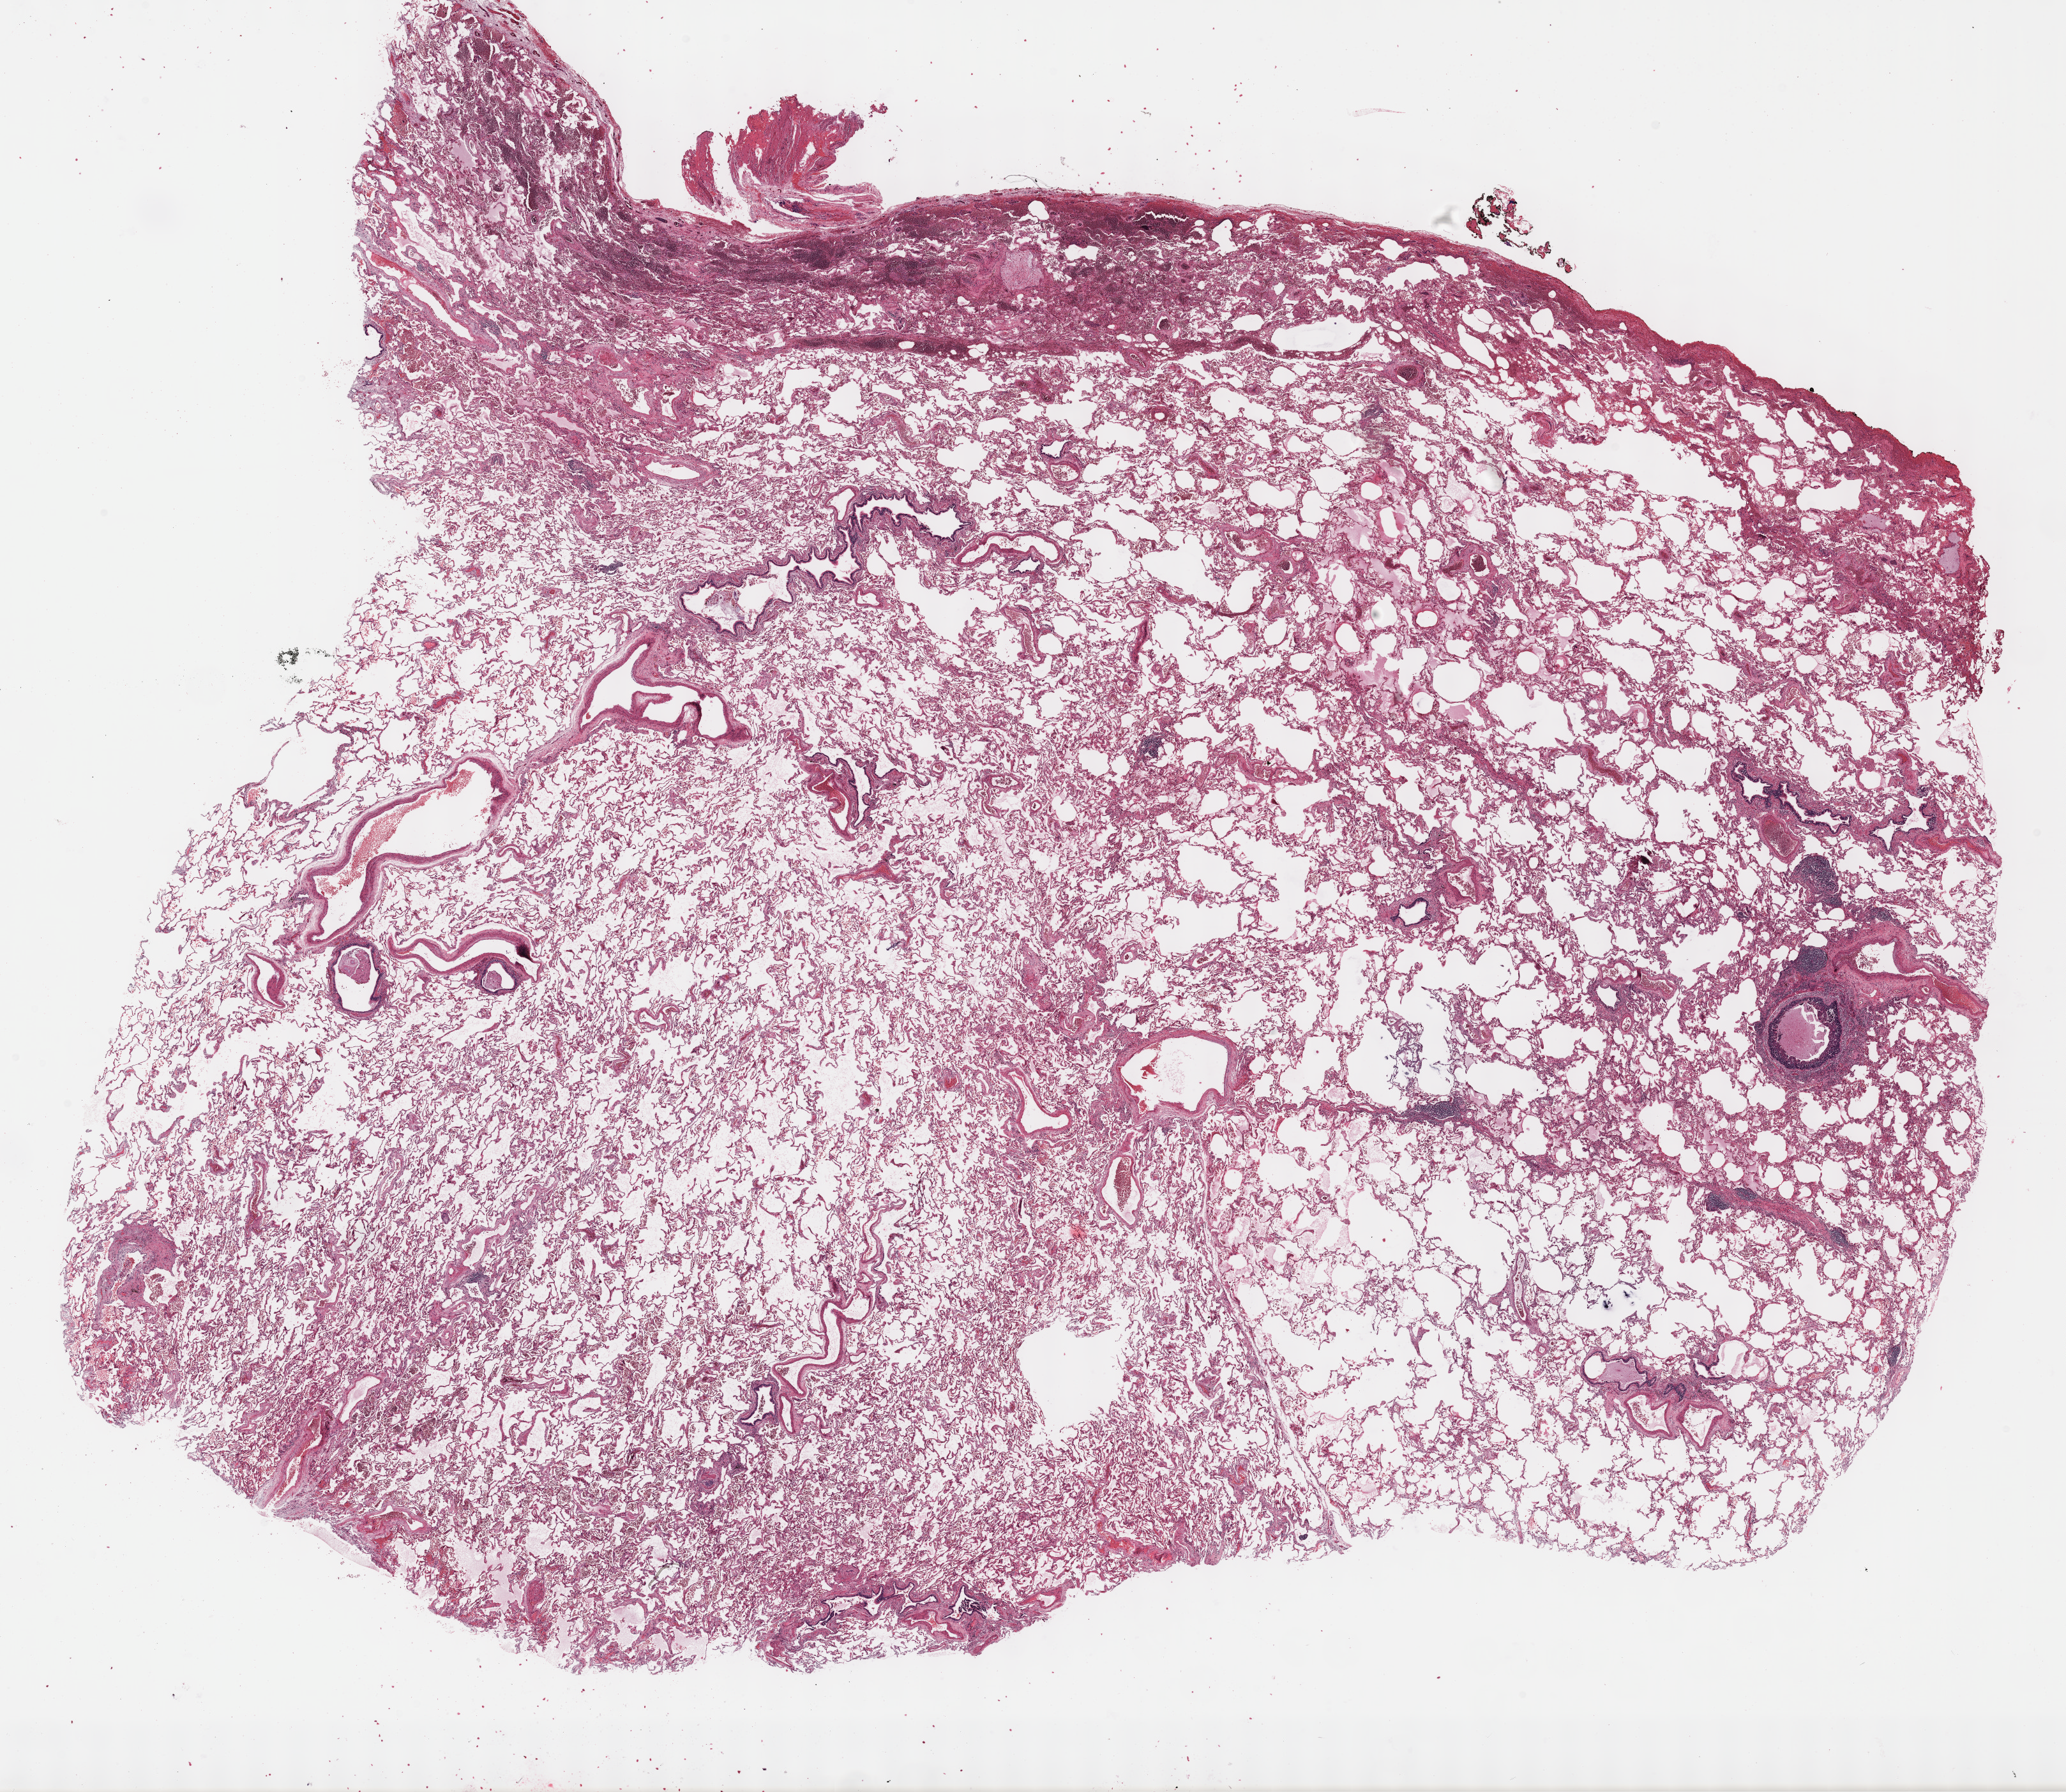
H&E whole-slide image — a low-resolution overview of the entire scanned area, about 26.2 x 22.7 mm (acquisition: 40x scan), formalin-fixed paraffin-embedded (FFPE) diagnostic section, primary tumour sample from the lung. Patient: female, age at initial diagnosis 71 years.
AJCC pathologic stage: III (6th edition). Laterality: right. Histologic diagnosis: Squamous cell carcinoma, NOS (middle lobe, lung). TNM: T3 N1 MX.